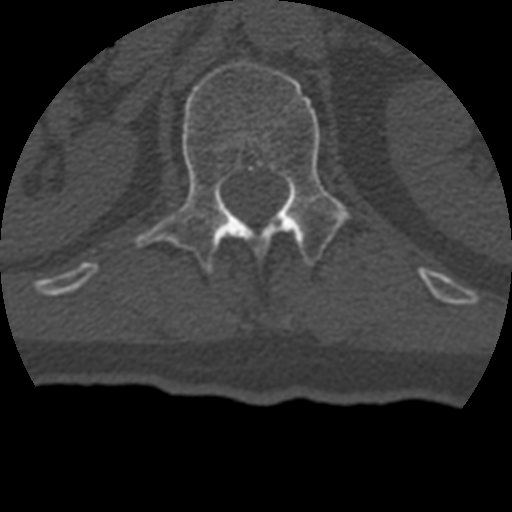
CT including the spine, one axial slice; slice 149 of 399 in the series (ordered by position); 120 kVp; bone window (W 1800 / L 400 HU); 1.25 mm slice thickness; 512 × 512 image matrix. Patient age 69 years. From the clinical record (not read from this slice): primary cancer: prostate.
Annotated regions visible in this slice (semi-automatic segmentation, software-assisted and operator-edited):
- L1 vertebra: box from (x=135, y=61) to (x=351, y=275) px